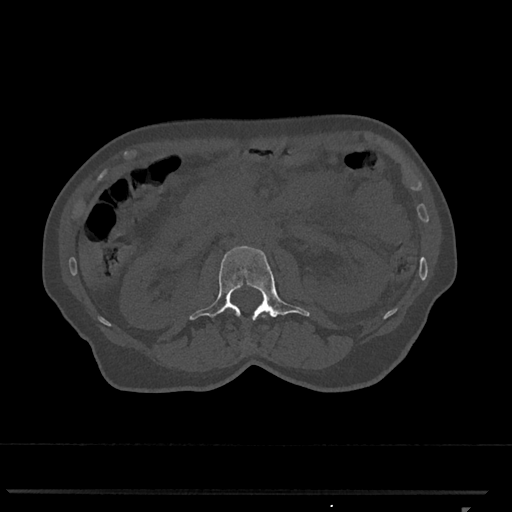
CT including the spine, one axial slice. Position 348 of 793 along the scan axis. 120 kVp. Bone window (W 1800 / L 400 HU). 0.5 mm slice thickness. 512 × 512 image matrix, field of view 380 × 380 mm. Female patient, age 62 years. From the clinical record (not read from this slice): primary cancer: renal.
Annotated regions visible in this slice (semi-automatically segmented with operator editing):
- L1 vertebra: bounding box <262,315,266,318> (left, top, right, bottom; pixels)
- L2 vertebra: <189,246,310,320>